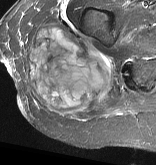
MRI of an extremity soft-tissue mass, one axial slice; position 23 of 57 along the scan axis; STIR; MR volume resampled by the dataset authors to the PET/CT grid (not the native acquisition matrix); 3.27 mm slice thickness; 156 × 165 image matrix, field of view 152 × 161 mm. Female patient. From the clinical record (not read from this slice): histological type: epithelioid sarcoma with vascular differentiation; site of the primary tumour: right buttock.
Outlined on this slice (expert contour drawn on MRI and transferred to this co-registered scan by the dataset authors):
- gross tumour volume (mass): bounding box <26,25,114,116> (left, top, right, bottom; pixels)